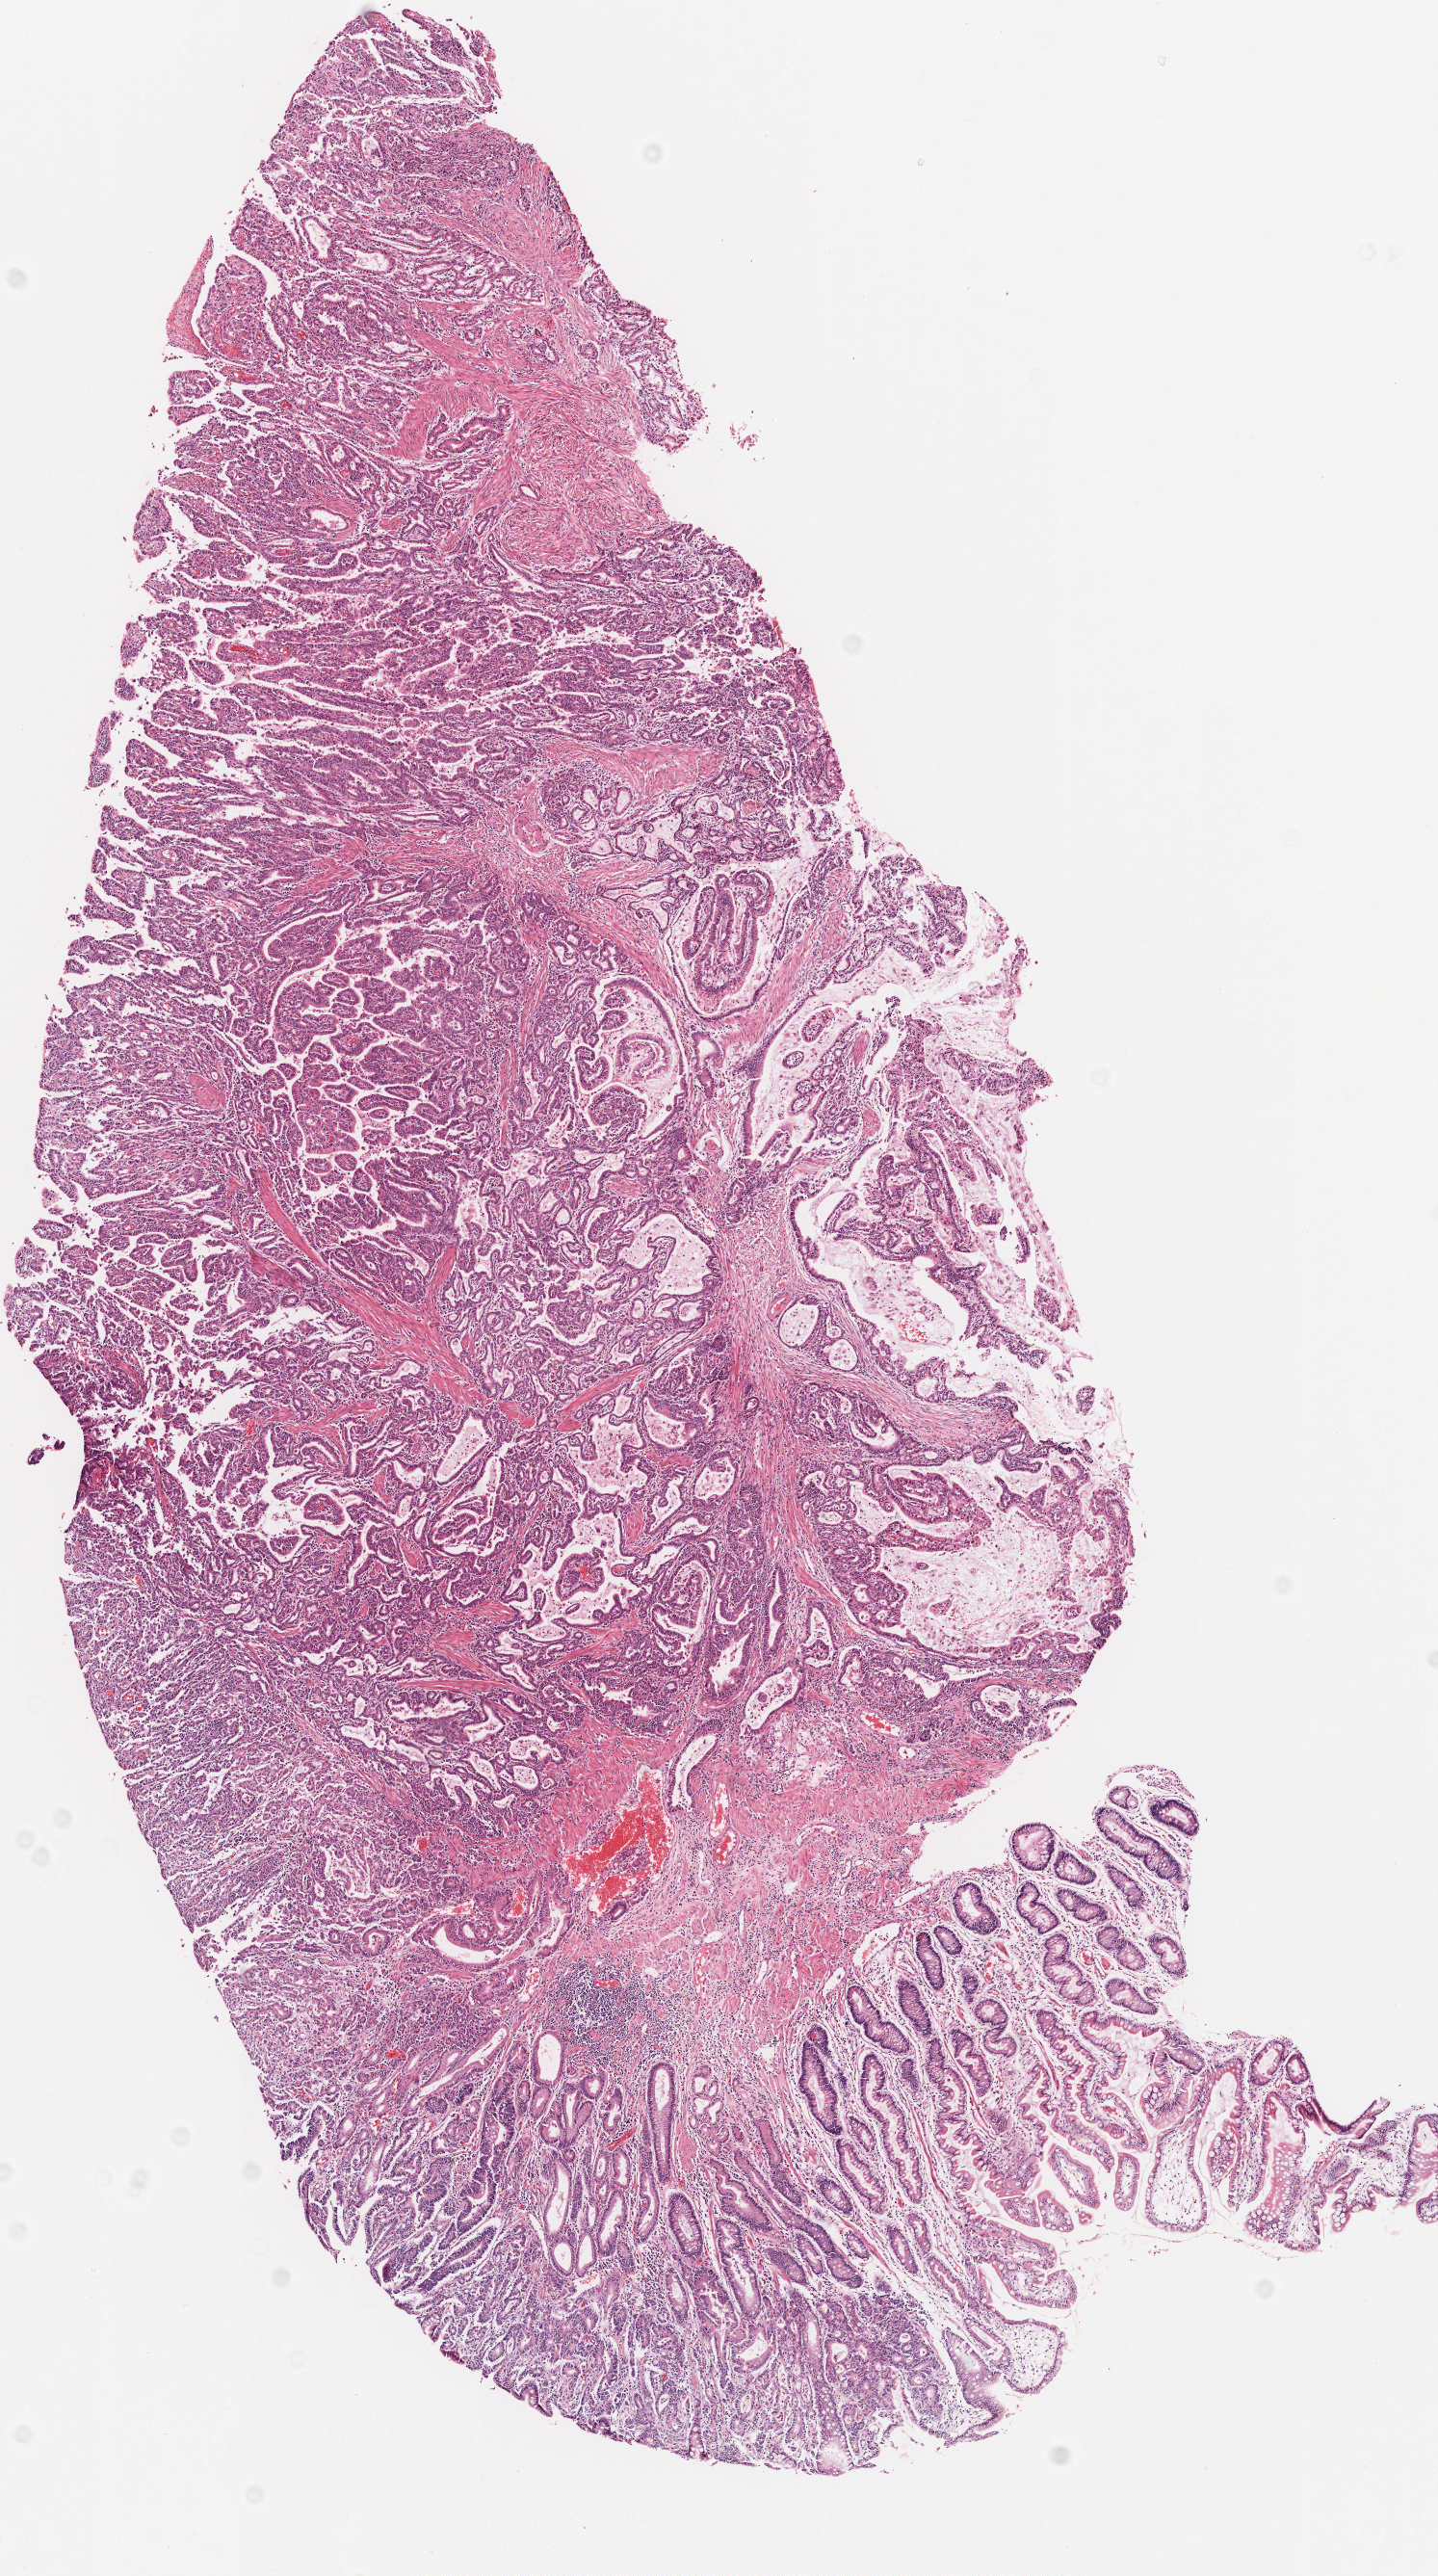
H&E-stained whole-slide image — shown as a low-resolution overview of the whole scanned area (about 5.9 x 10.6 mm). FFPE section. Sample: primary tumour, stomach. Male, age 54 years at initial diagnosis. Histologic grade: G2 (moderately differentiated).
TNM: T2 N2 M0. Pathologic diagnosis: Tubular adenocarcinoma (gastric antrum). Lymph nodes positive (case pathology): 5 of 53 examined. AJCC pathologic stage: IIB.